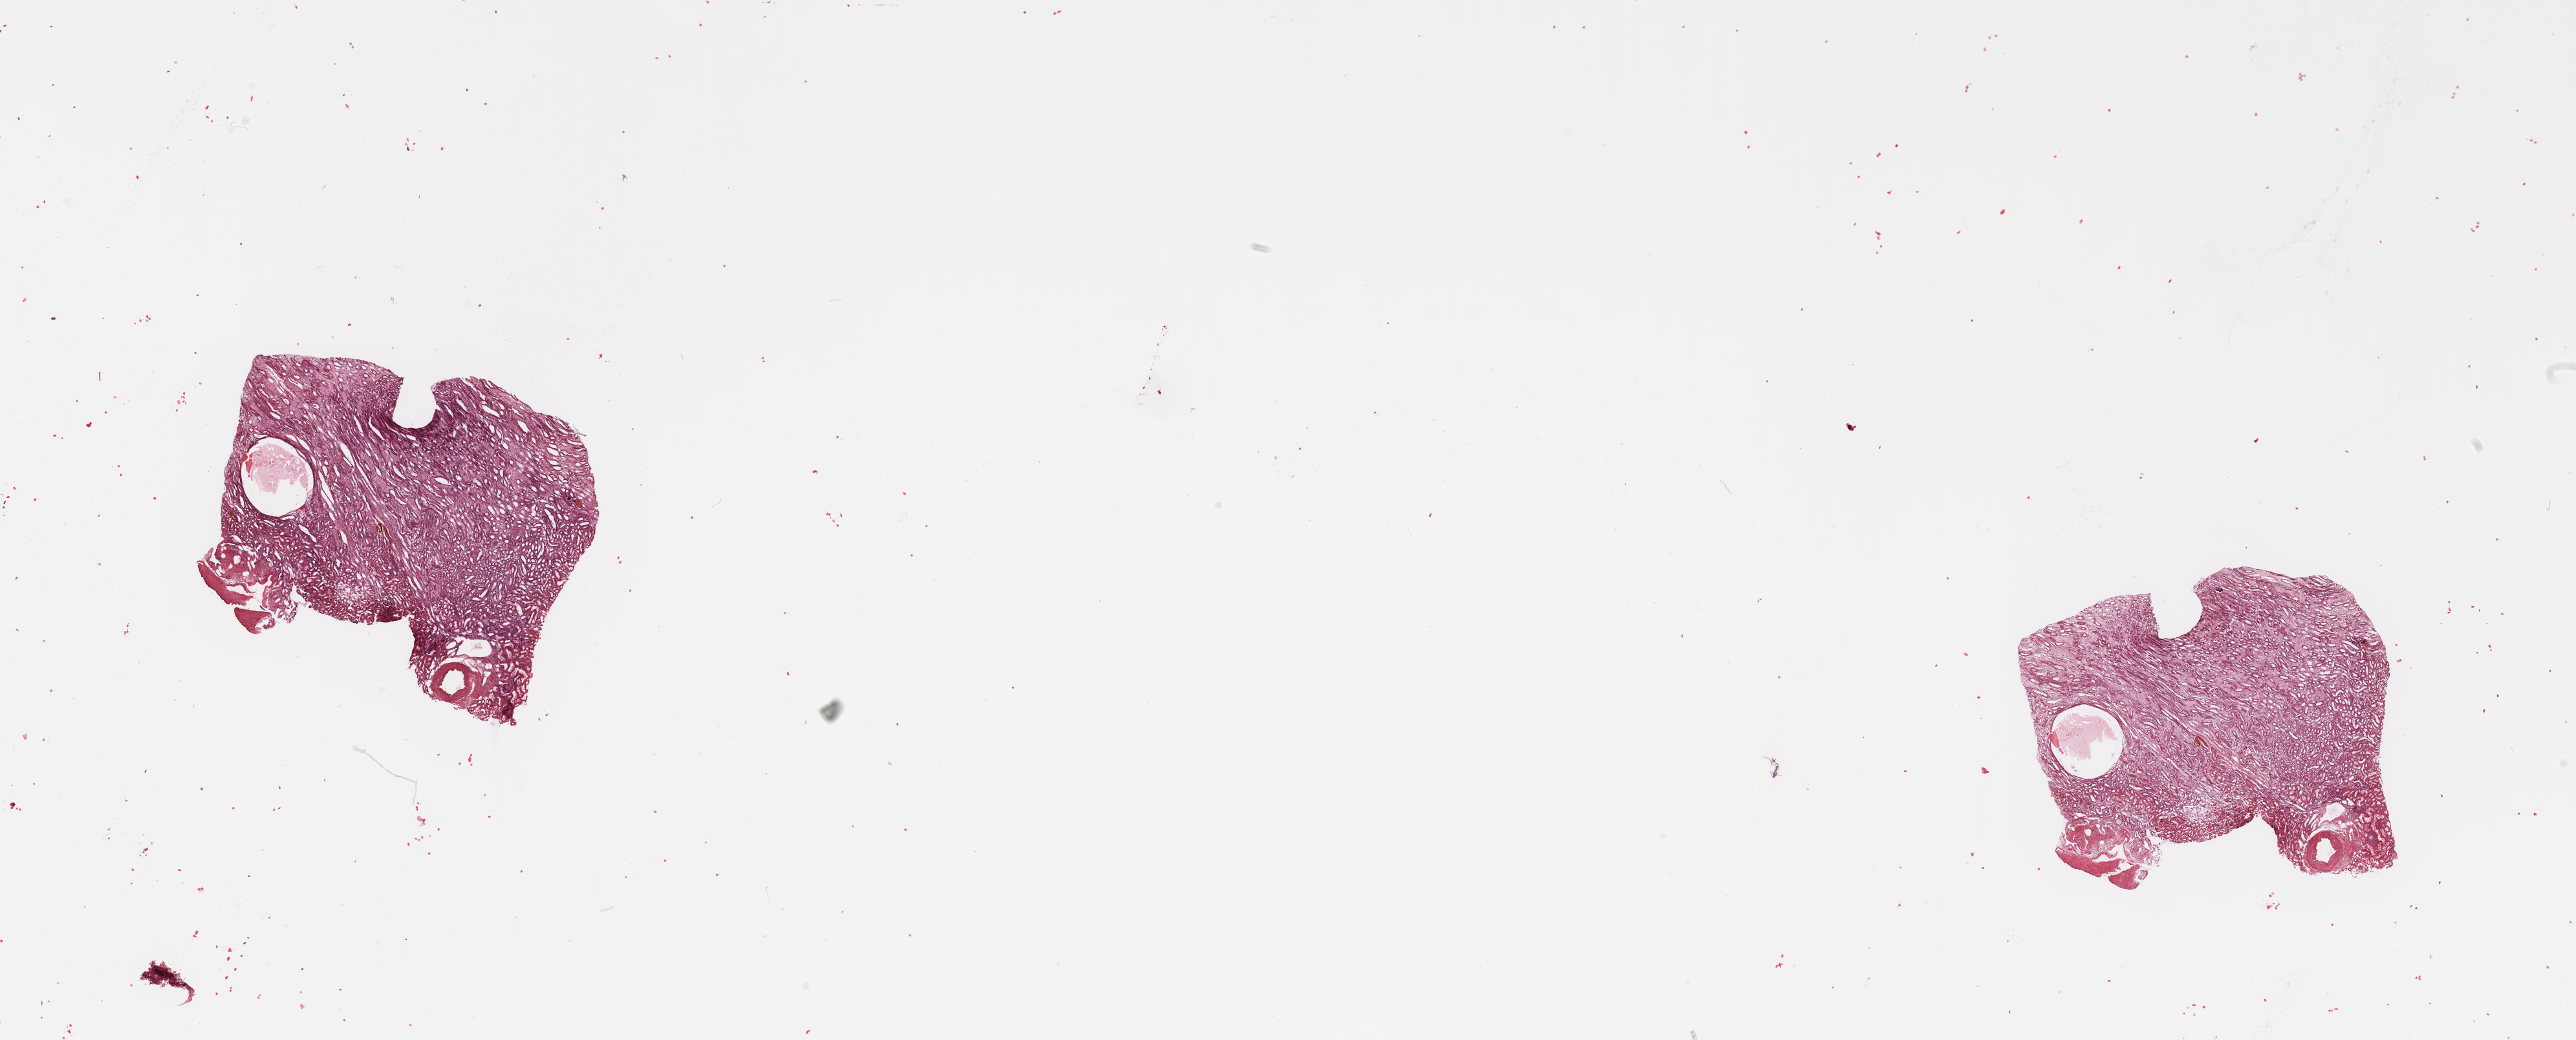
Digitized H&E tissue section (whole slide) — shown as a low-resolution overview of the whole scanned area (about 31.5 x 12.7 mm); normal (non-tumour) tissue sample, sampled site: kidney. 67-year-old male patient.
* this section: normal (non-tumour) tissue from the same patient
* patient diagnosis: Renal cell carcinoma, NOS